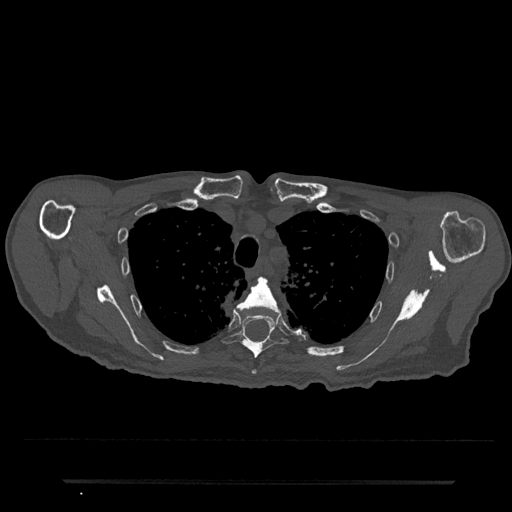
CT including the spine, one axial slice. Position 591 of 797 along the scan axis. Reconstruction kernel Br40s/3. Bone window (W 1800 / L 400 HU). 512 × 512 image matrix, field of view 427 × 427 mm. Patient: male, 74 years. From the clinical record (not read from this slice): primary cancer: prostate.
Outlined on this slice (semi-automatically segmented with operator editing):
- T4 vertebra: box from (x=237, y=277) to (x=282, y=374) px
- T5 vertebra: (x=219, y=304)–(x=289, y=359)